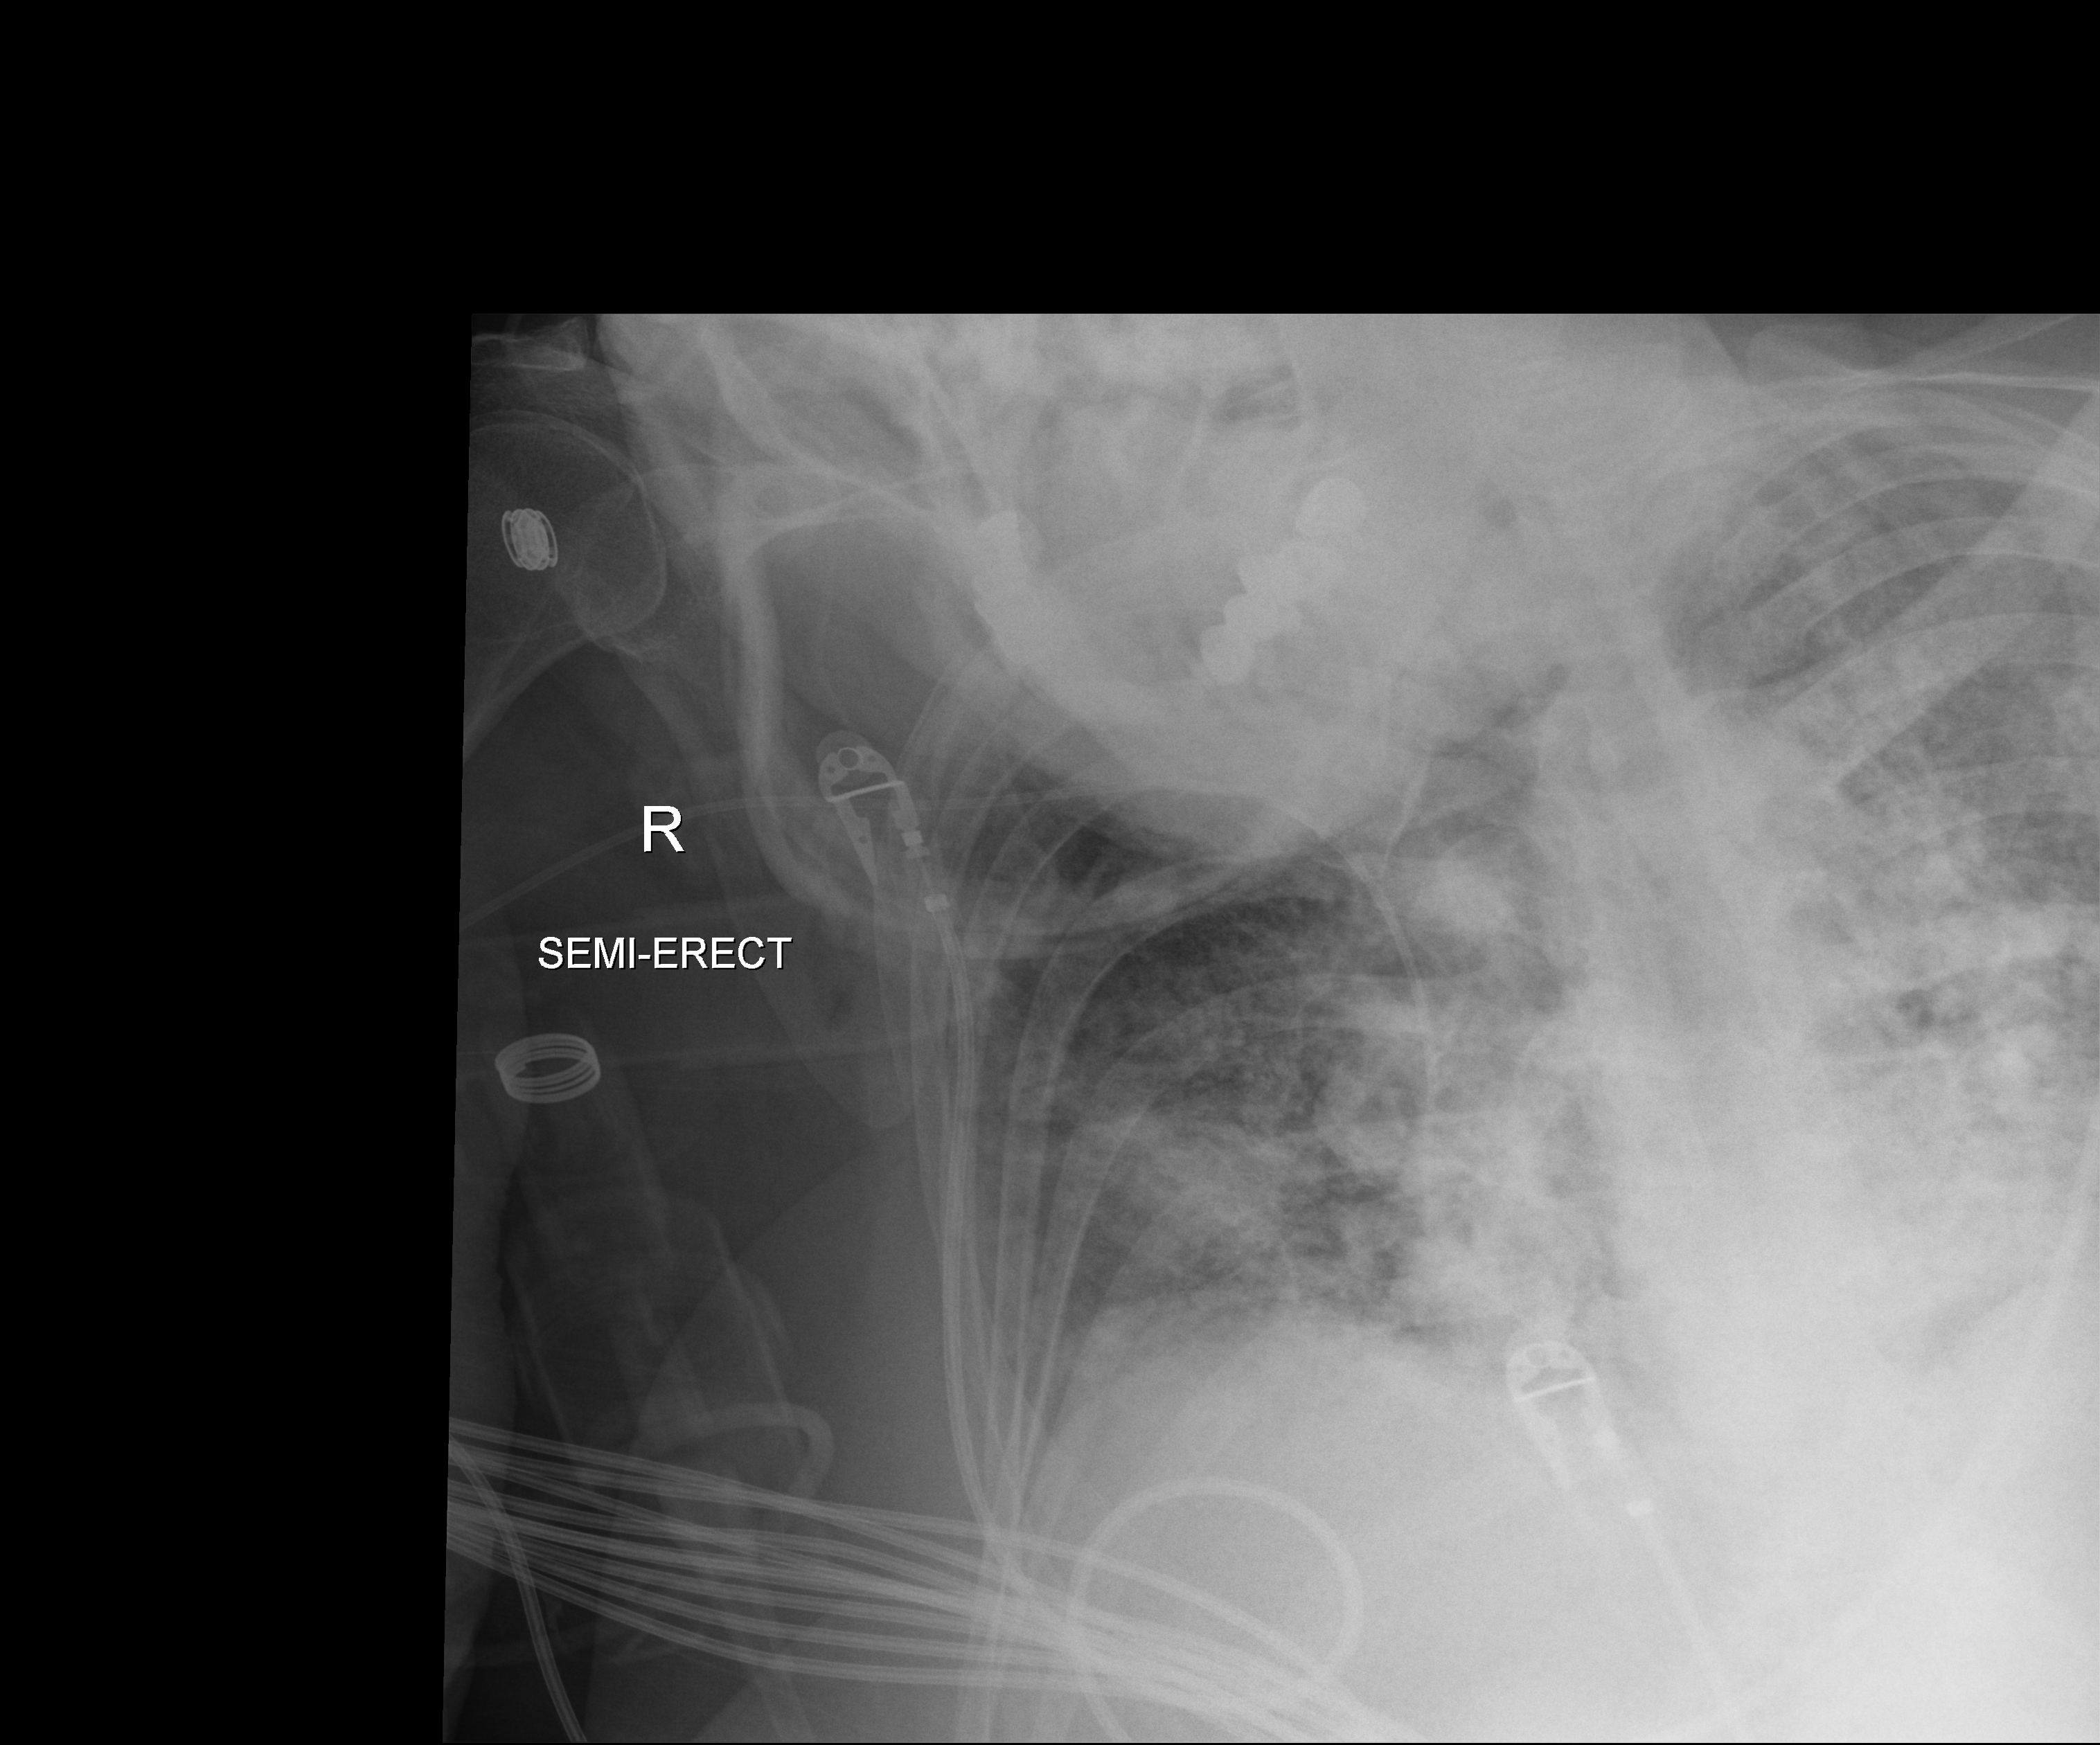
Chest X-ray (portable), anteroposterior (AP) projection. Patient hospitalised with COVID-19; female, aged 60–74 years.
Admission-level facts for this patient (not findings on this image; timing relative to this image not recorded): admitted to intensive care during this hospital stay: yes; mechanically ventilated during this hospital stay: yes.